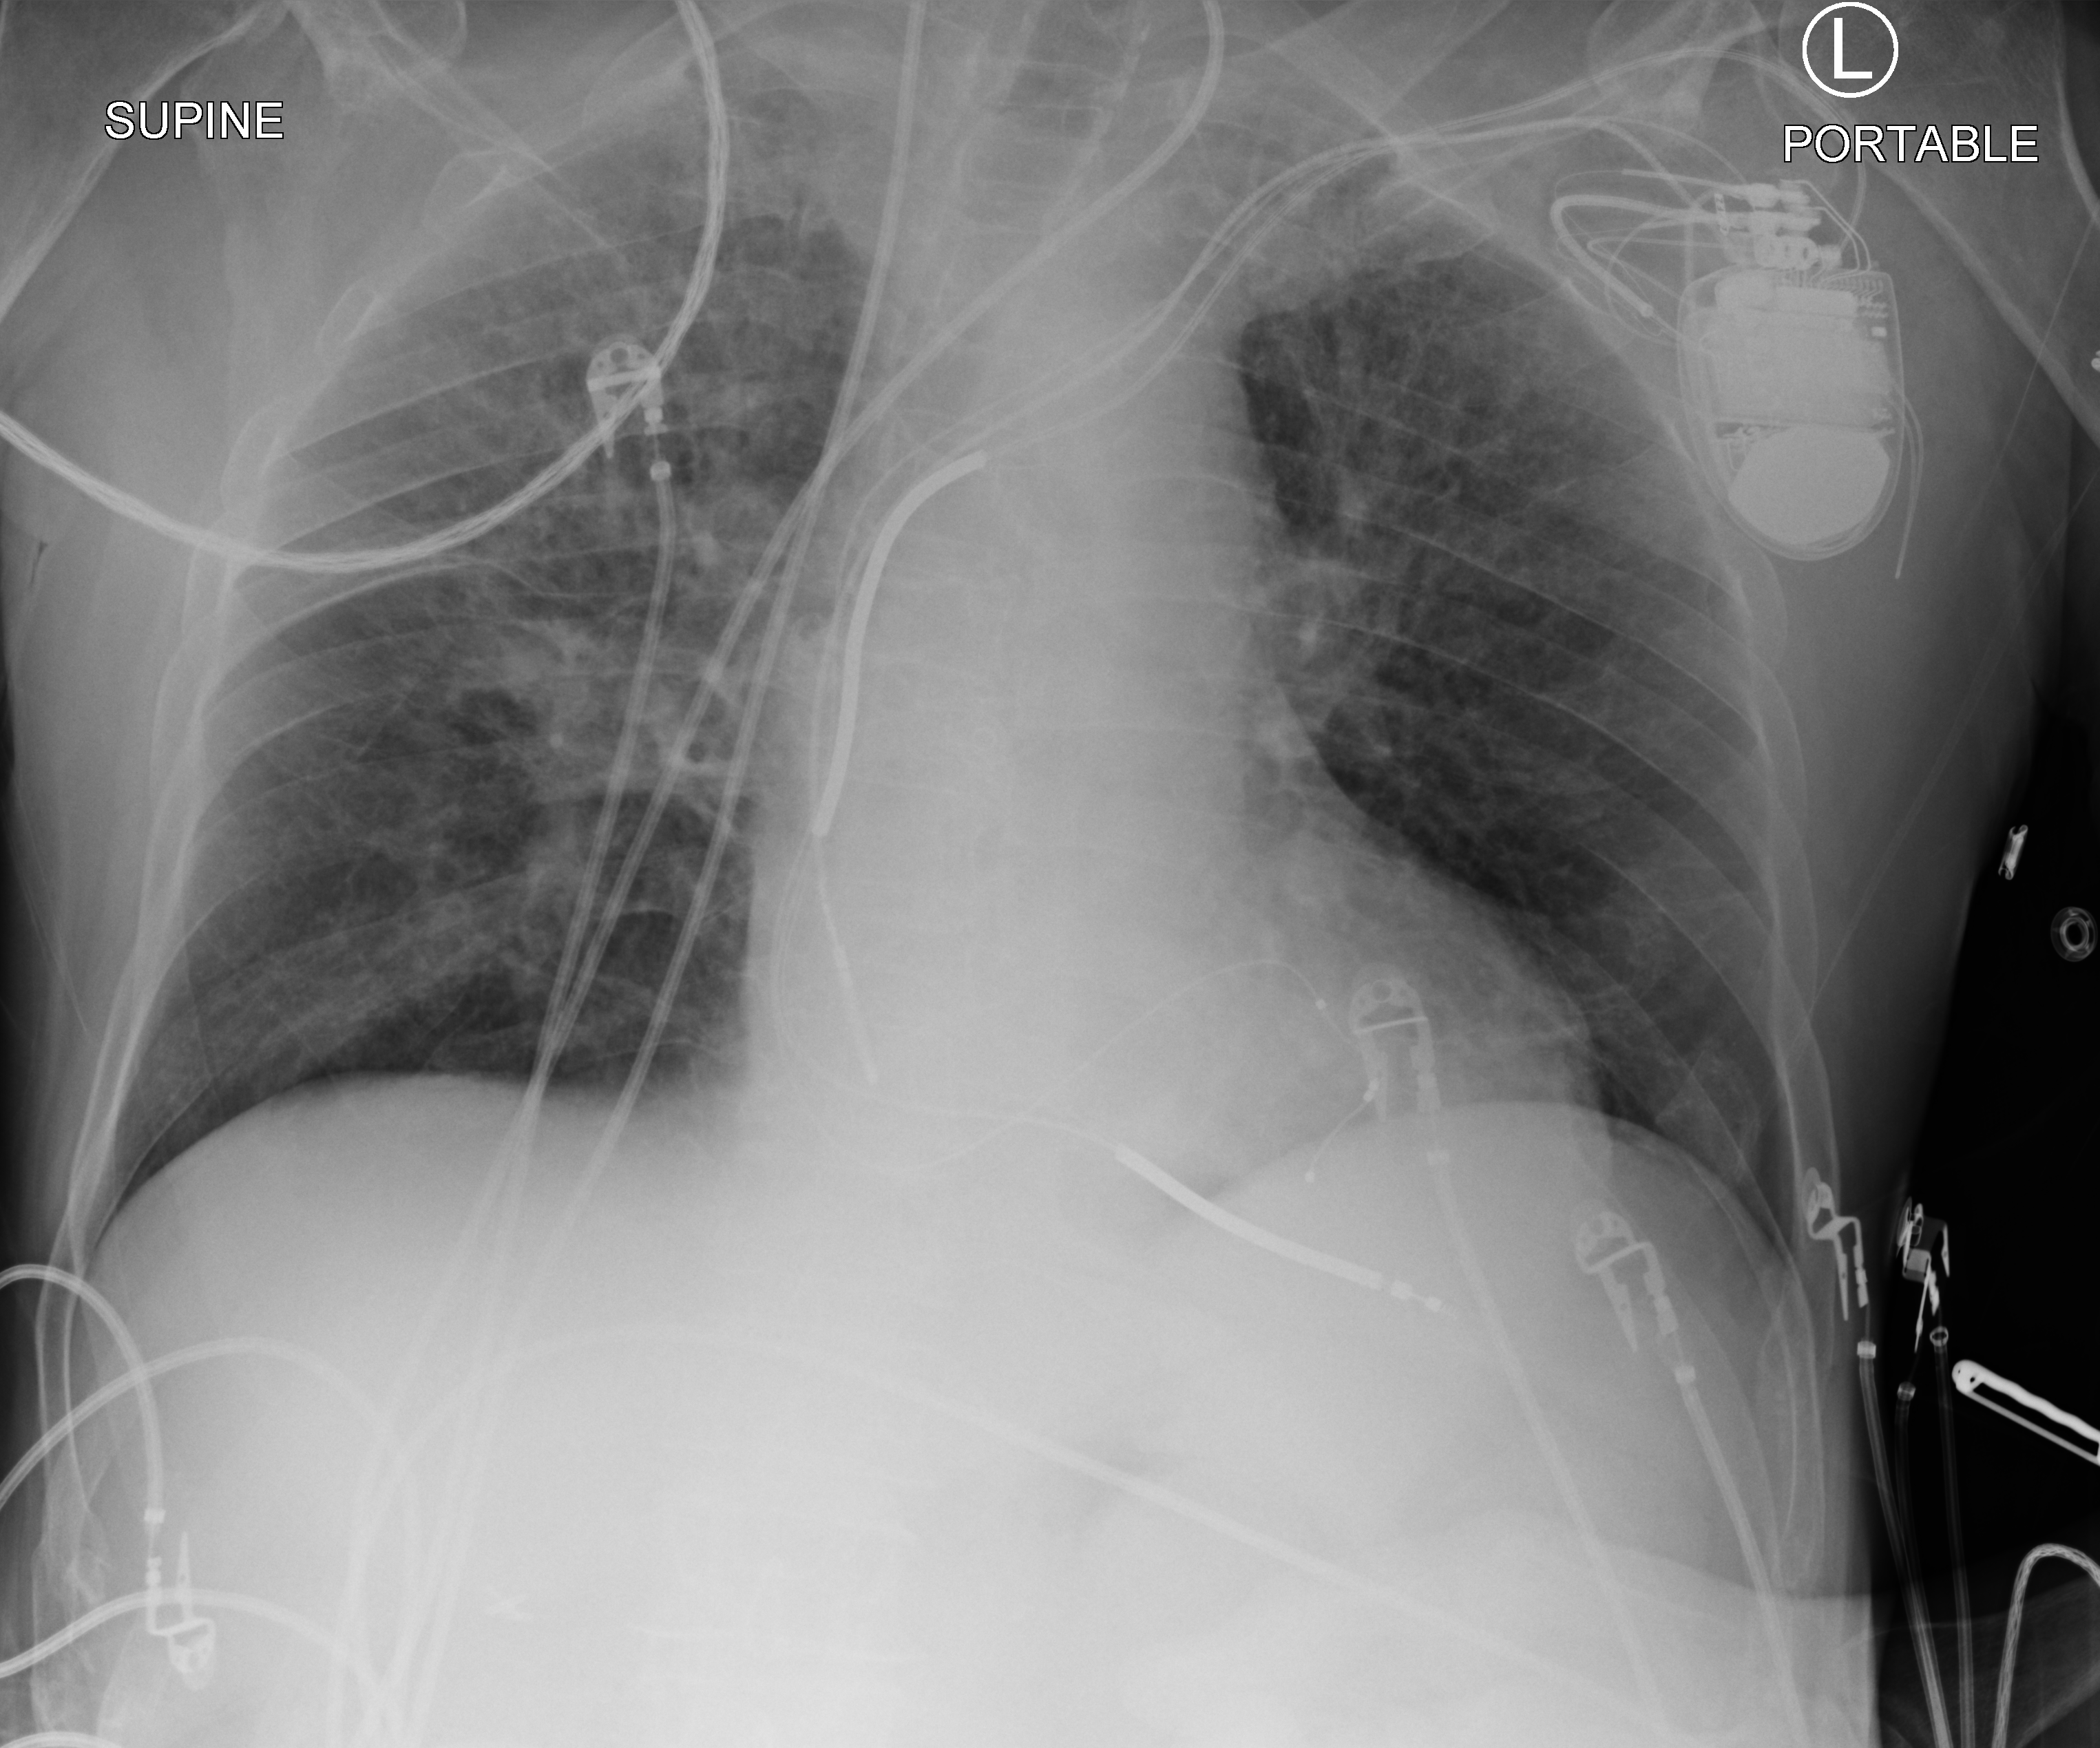
Bedside chest radiograph (computed radiography); anteroposterior (AP) projection. Patient hospitalised with COVID-19; male, aged 75–90 years.
Admission-level facts for this patient (not findings on this image; timing relative to this image not recorded): admitted to intensive care during this hospital stay: no; mechanically ventilated during this hospital stay: no.